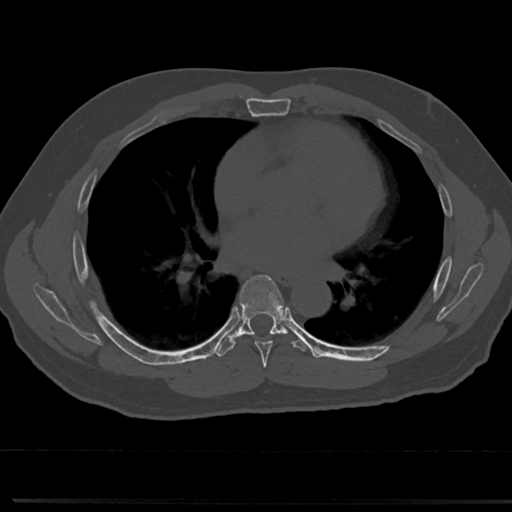
CT including the spine, one axial slice; position 425 of 817 along the scan axis; 120 kVp; bone window (W 1800 / L 400 HU); 0.5 mm slice thickness; 512 × 512 image matrix, field of view 355 × 355 mm. Patient: male, 61 years. Case-level facts recorded for this patient, not image findings: primary cancer: prostate.
Structures marked on this image (semi-automatic segmentation, software-assisted and operator-edited):
- T5 vertebra: box from (x=266, y=372) to (x=269, y=375) px
- T6 vertebra: (x=239, y=275)–(x=288, y=358)
- T7 vertebra: (x=240, y=325)–(x=285, y=335)